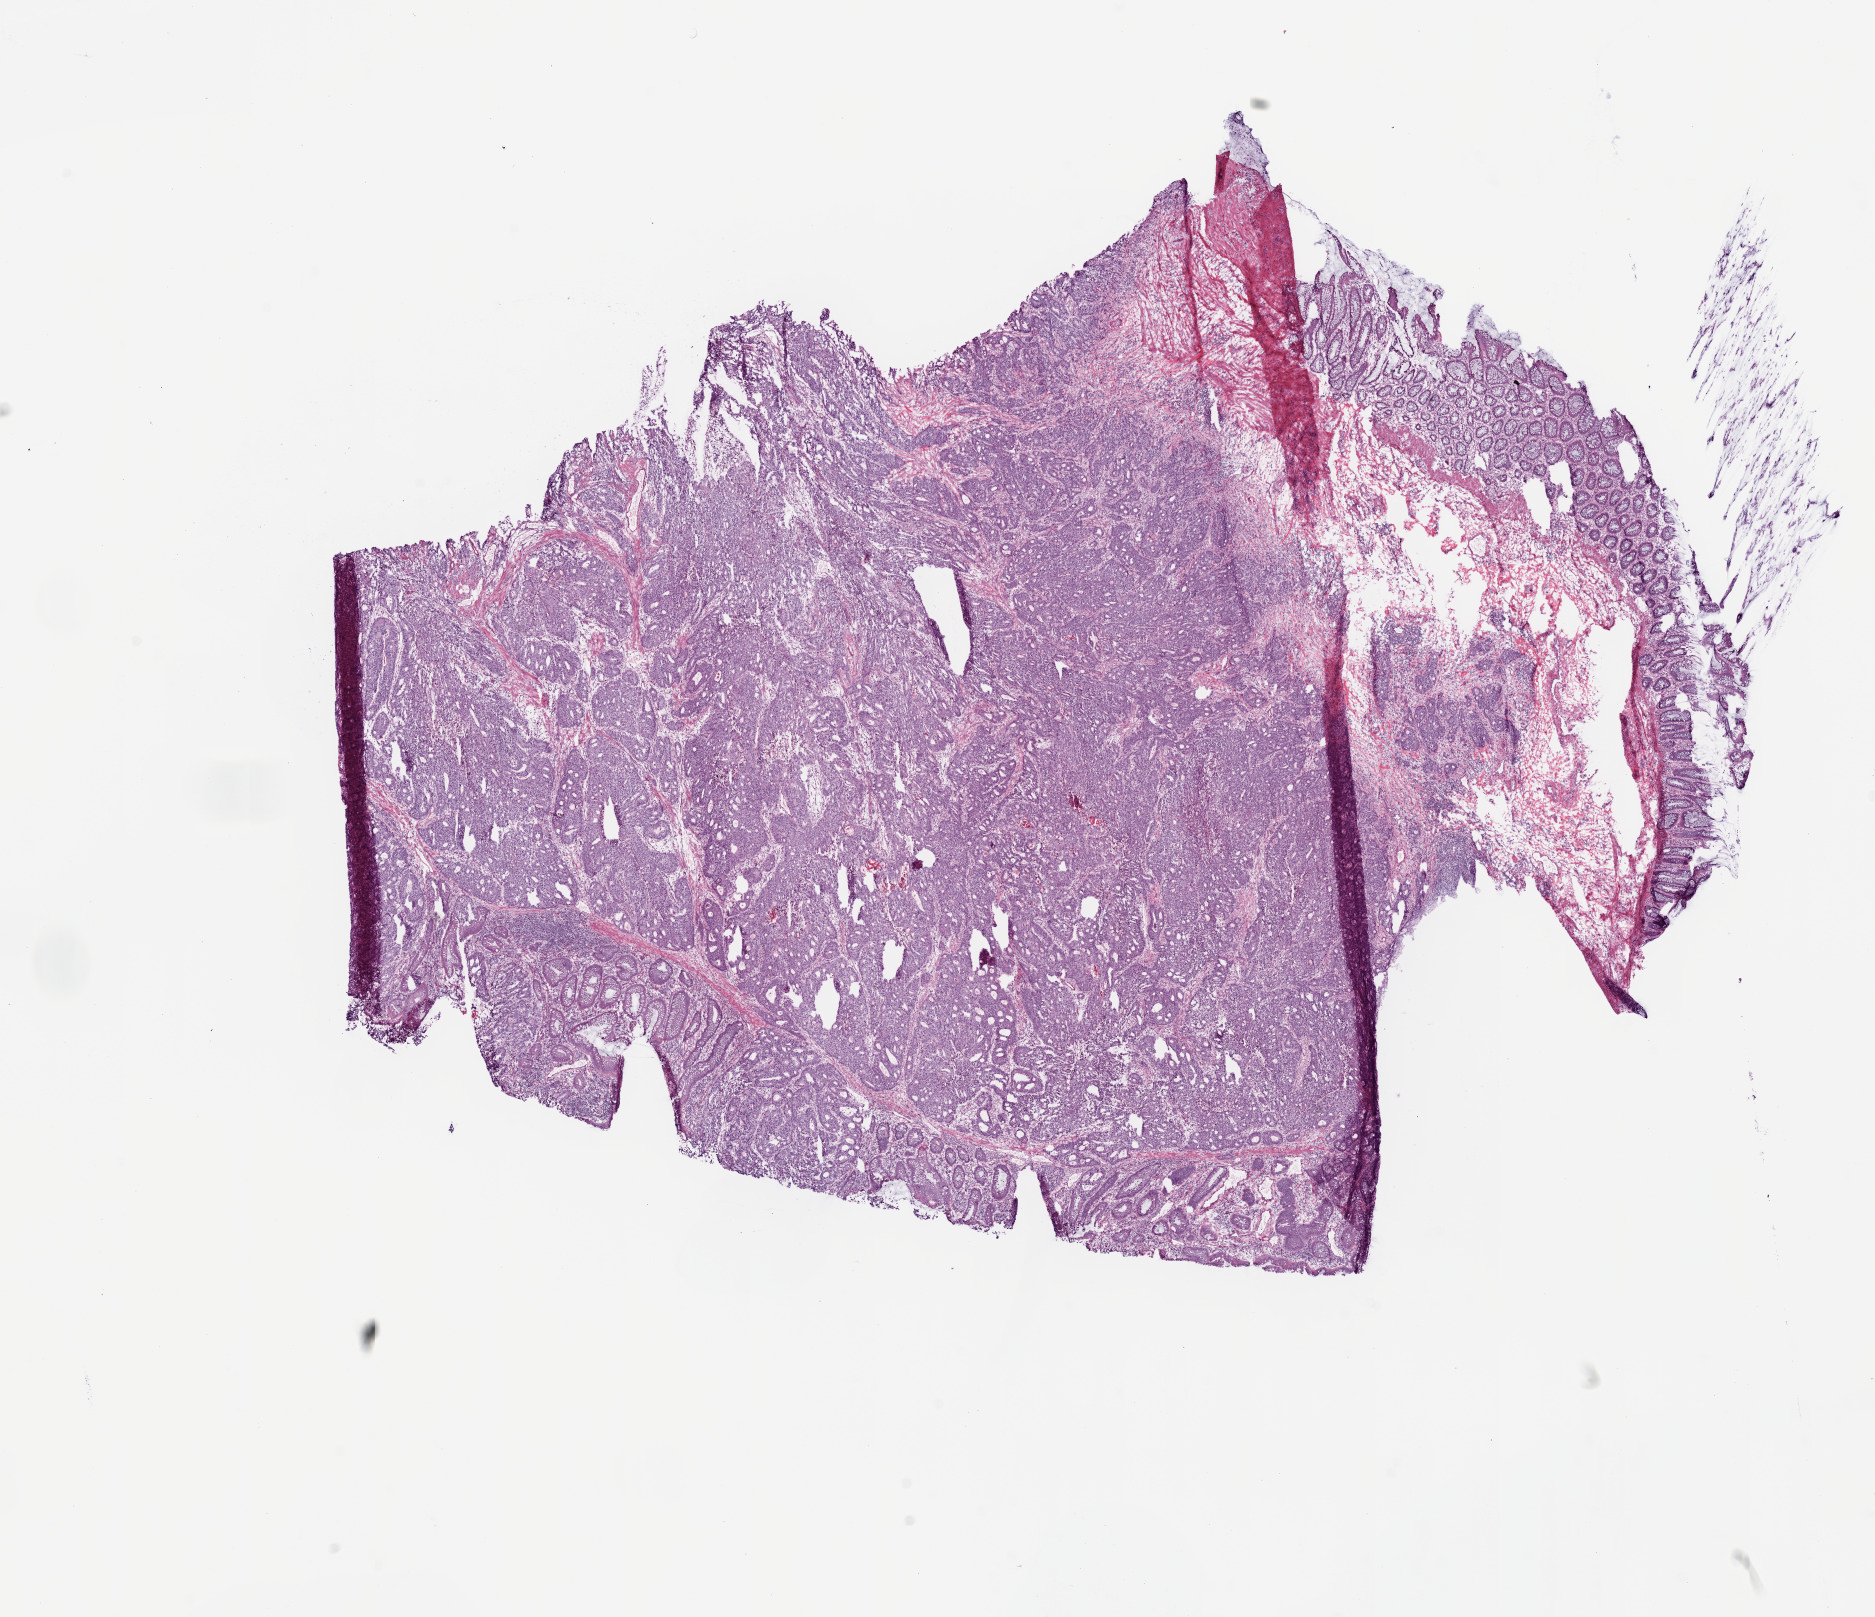
Whole-slide histology image, Hematoxylin and eosin (H&E) stained — whole scanned area (about 15.0 x 13.0 mm, from a 20x scan) shown as a low-resolution overview. Frozen section from the bottom of the tissue portion. Rectum, primary tumour sample. Patient: male, age at initial diagnosis 60 years. Slide review estimates, as recorded: tumour cells 75%, tumour nuclei 75%, normal cells 15%, stromal cells 5%, necrosis 5%.
AJCC pathologic stage: IV (6th edition). Pathologic diagnosis: Adenocarcinoma, NOS.